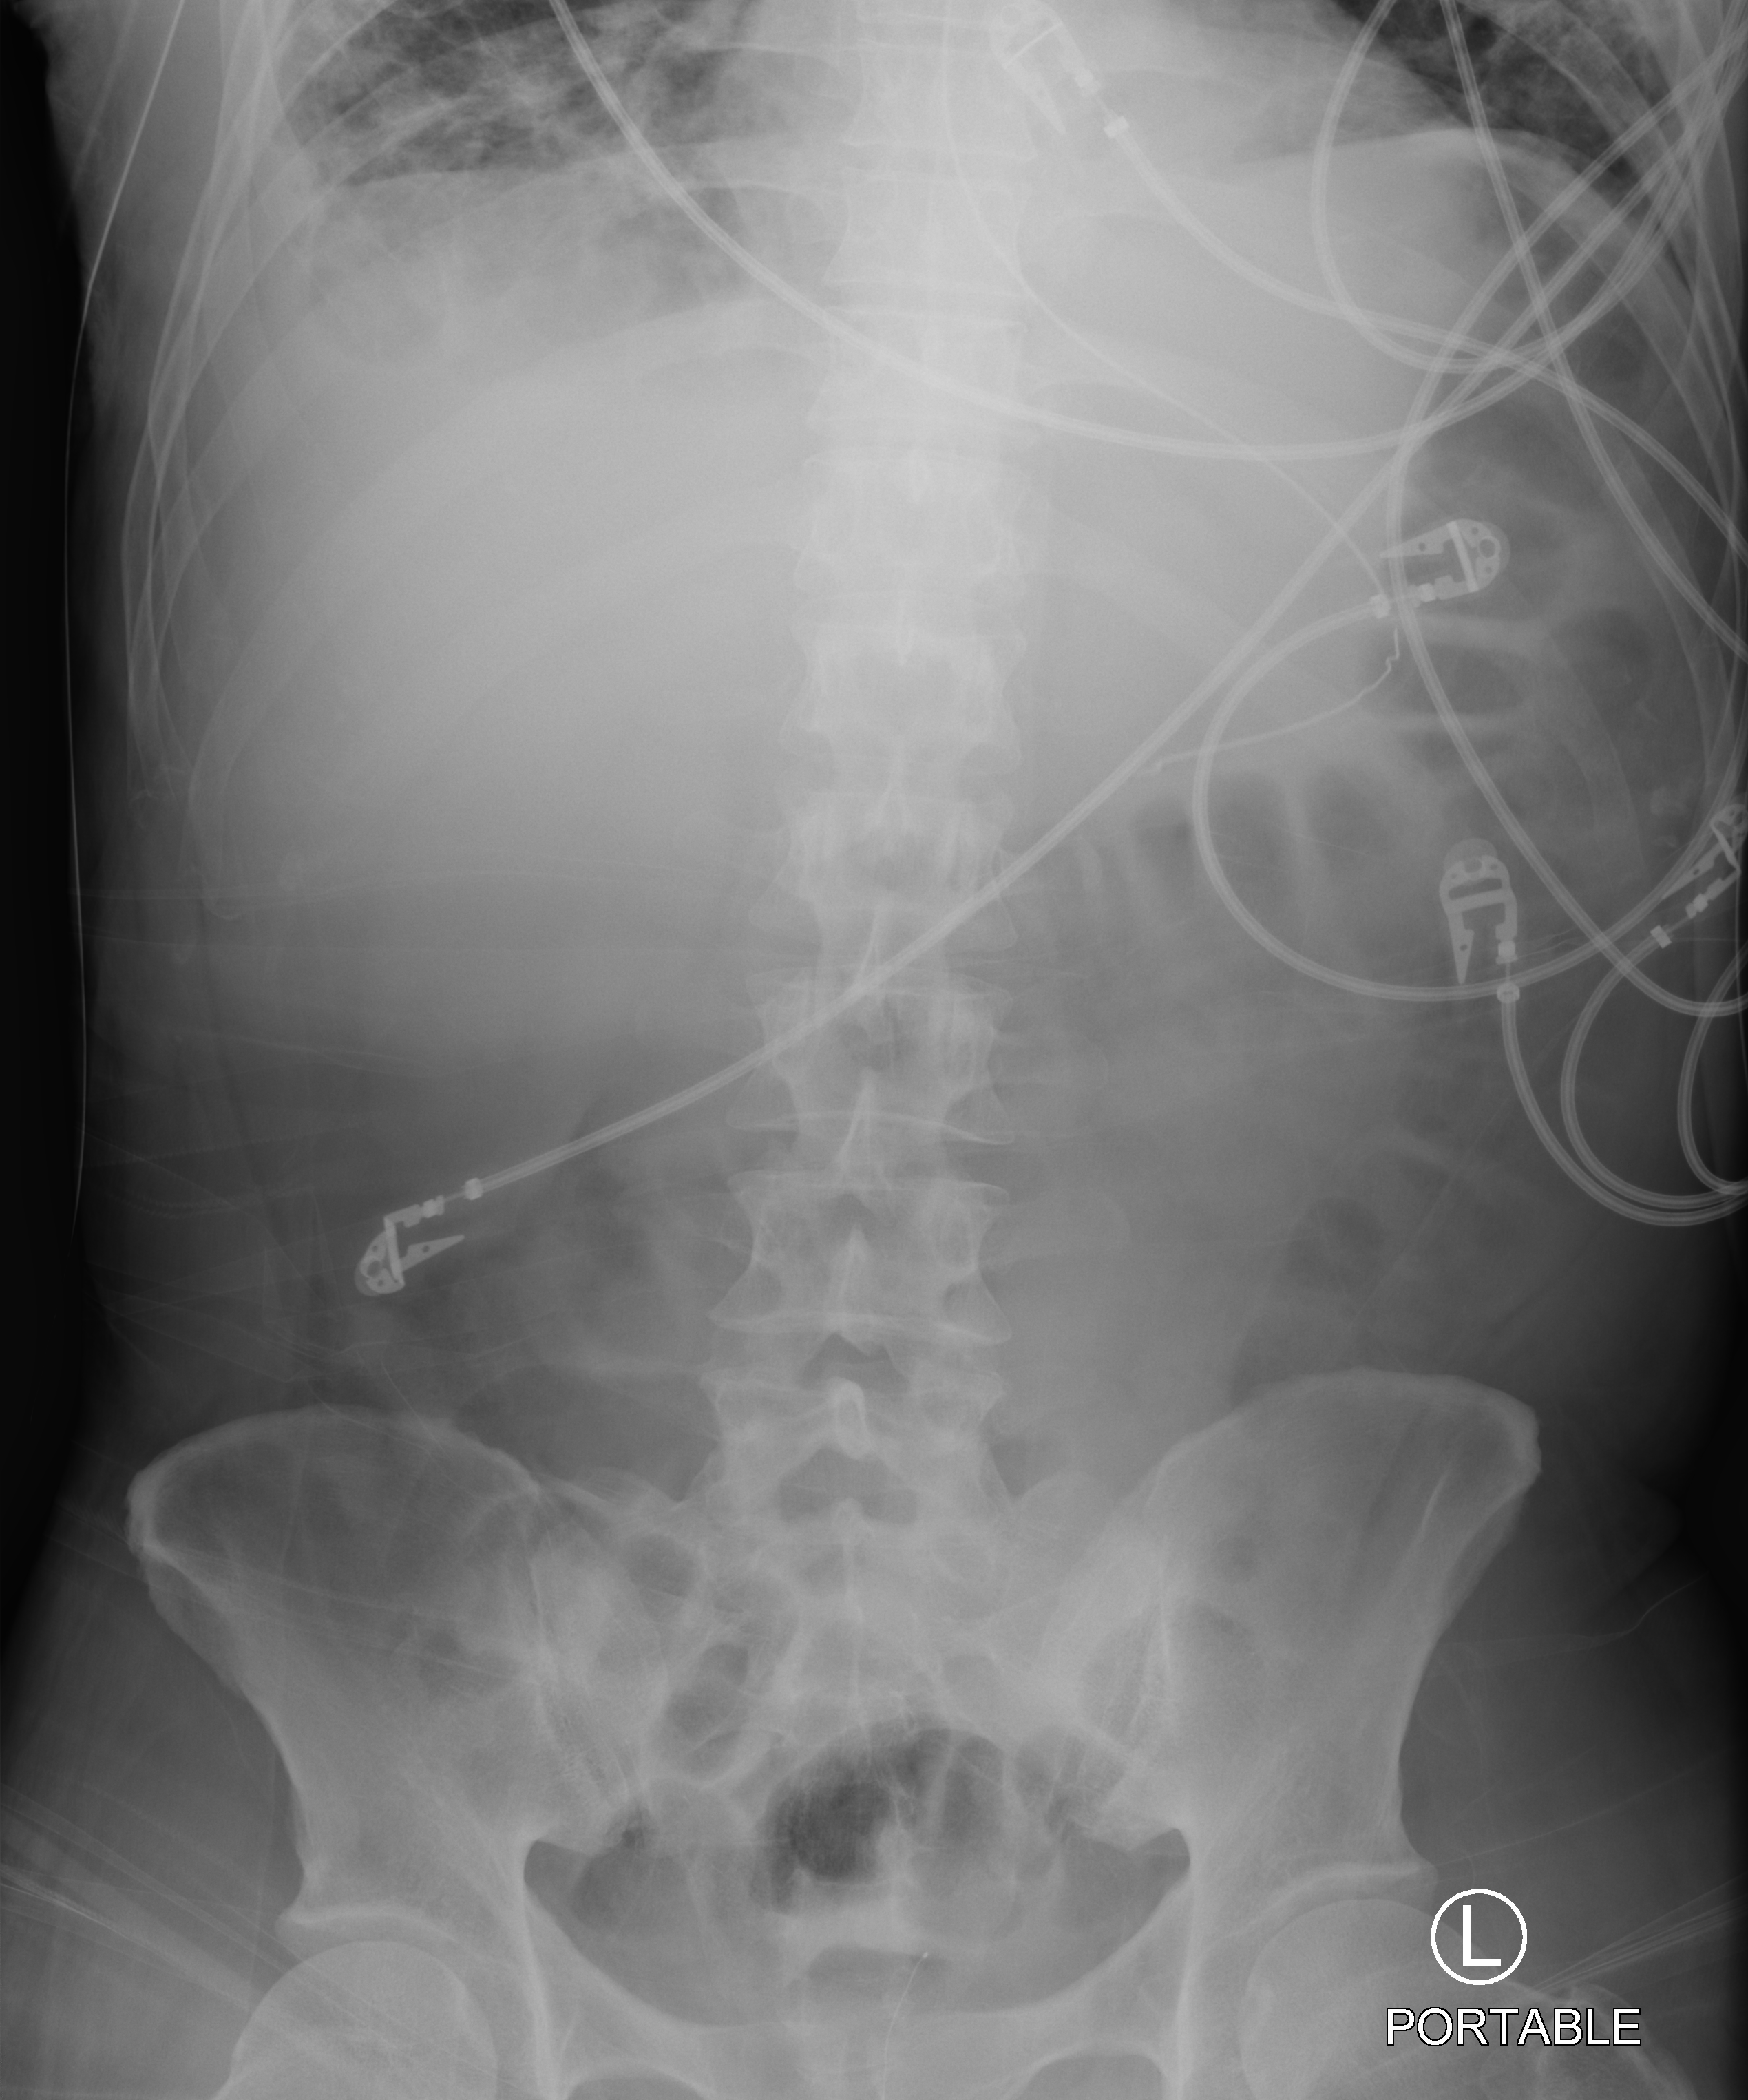
Portable abdomen radiograph; anteroposterior (AP) projection. Male patient hospitalised with COVID-19, age 18–59 years.
Hospital-stay facts (about this admission, not read from this image; timing relative to this image not recorded): length of hospital stay: 96 days; chronic kidney disease (admission record): no; admitted to intensive care during this hospital stay: yes.